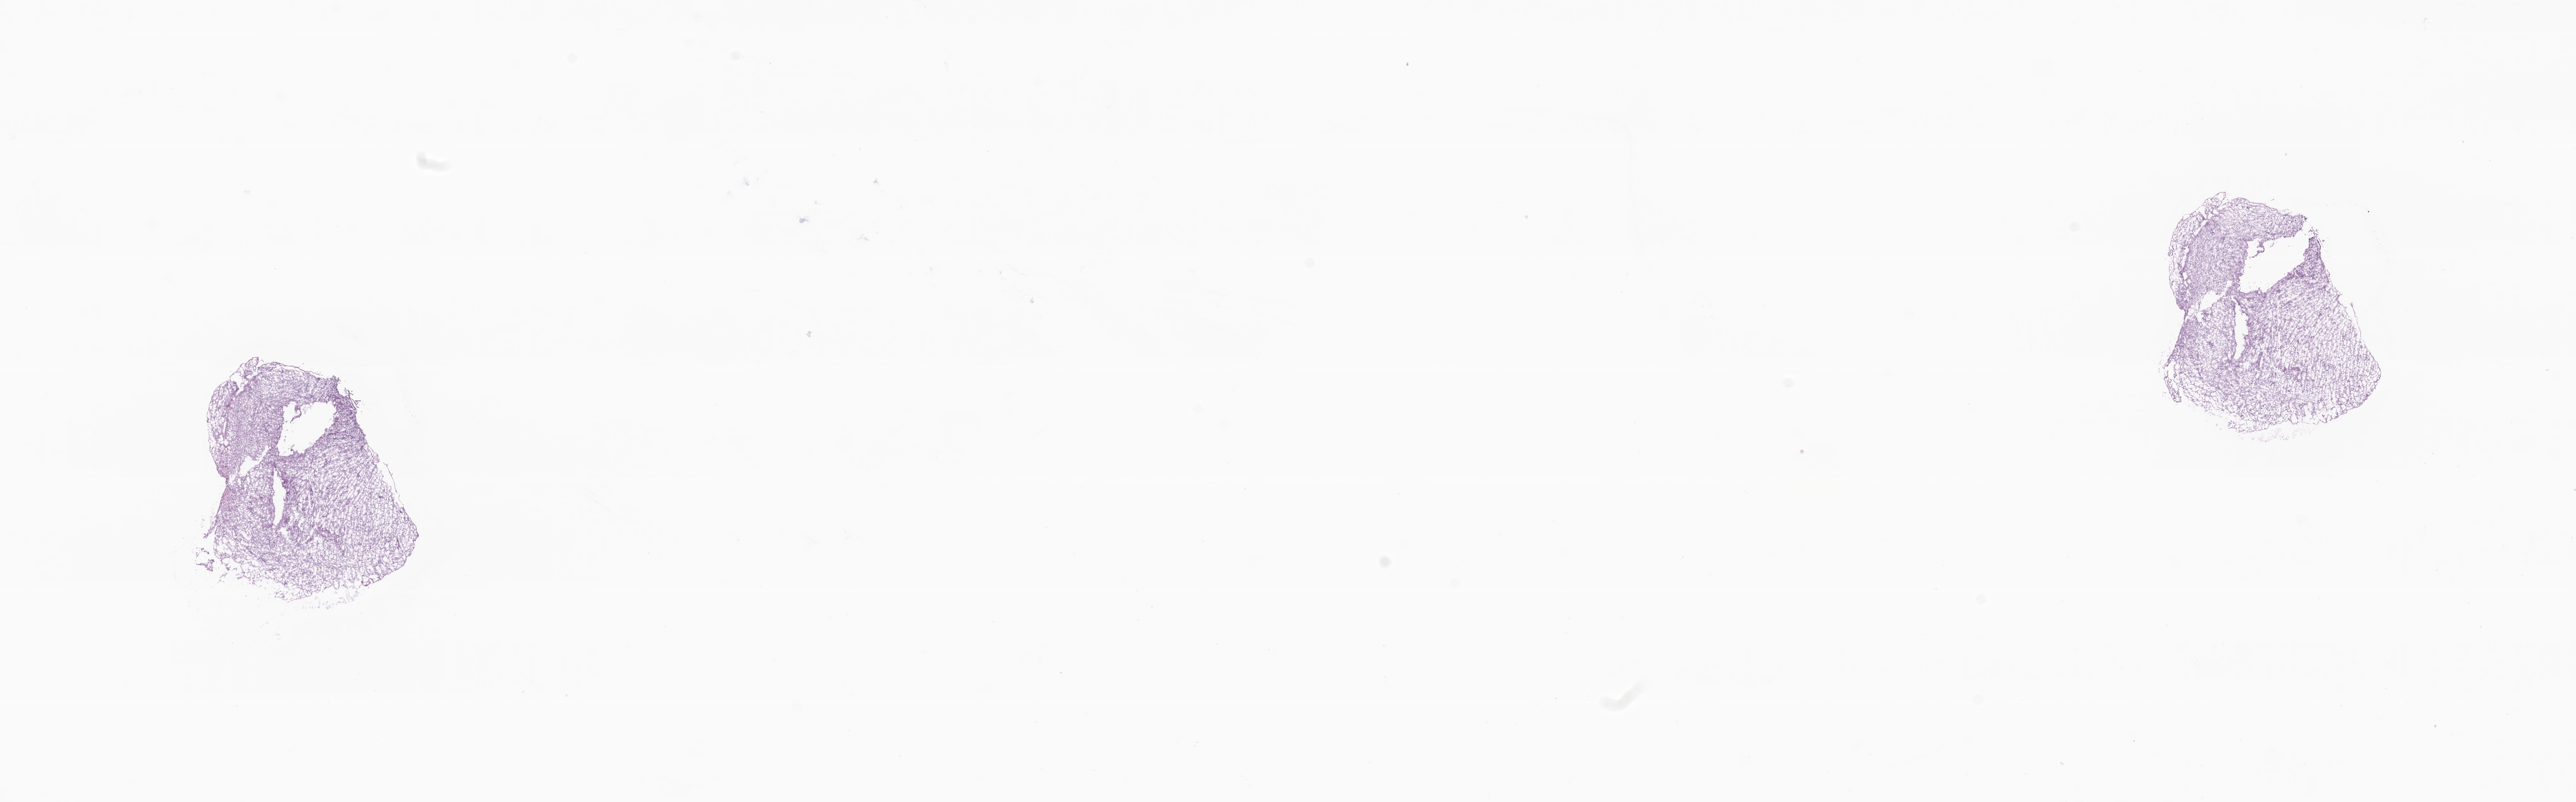
Whole-slide image, hematoxylin and eosin (H&E) stain of tumor tissue from the brain, shown as a low-resolution overview of the whole scanned area (about 24.7 x 7.7 mm). Frozen section (OCT-embedded). Patient: male, age 981 days (about 2.7 years).
Diagnosis: Astrocytoma, NOS.